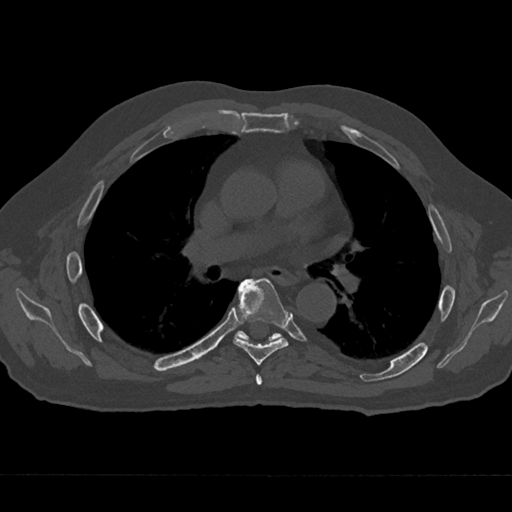
CT including the spine, one axial slice; slice 409 of 797 in the series (ordered by position); bone window (W 1800 / L 400 HU); 0.5 mm slice thickness; 512 × 512 image matrix, field of view 377 × 377 mm. Patient: male, 75 years. From the clinical record (not read from this slice): primary cancer: renal.
Structures marked on this image (semi-automatically segmented with operator editing):
- T5 vertebra: bounding box (x1, y1, x2, y2) in pixels: (256, 374, 262, 385)
- T6 vertebra: (233, 278, 289, 365)
- T7 vertebra: (237, 282, 280, 341)